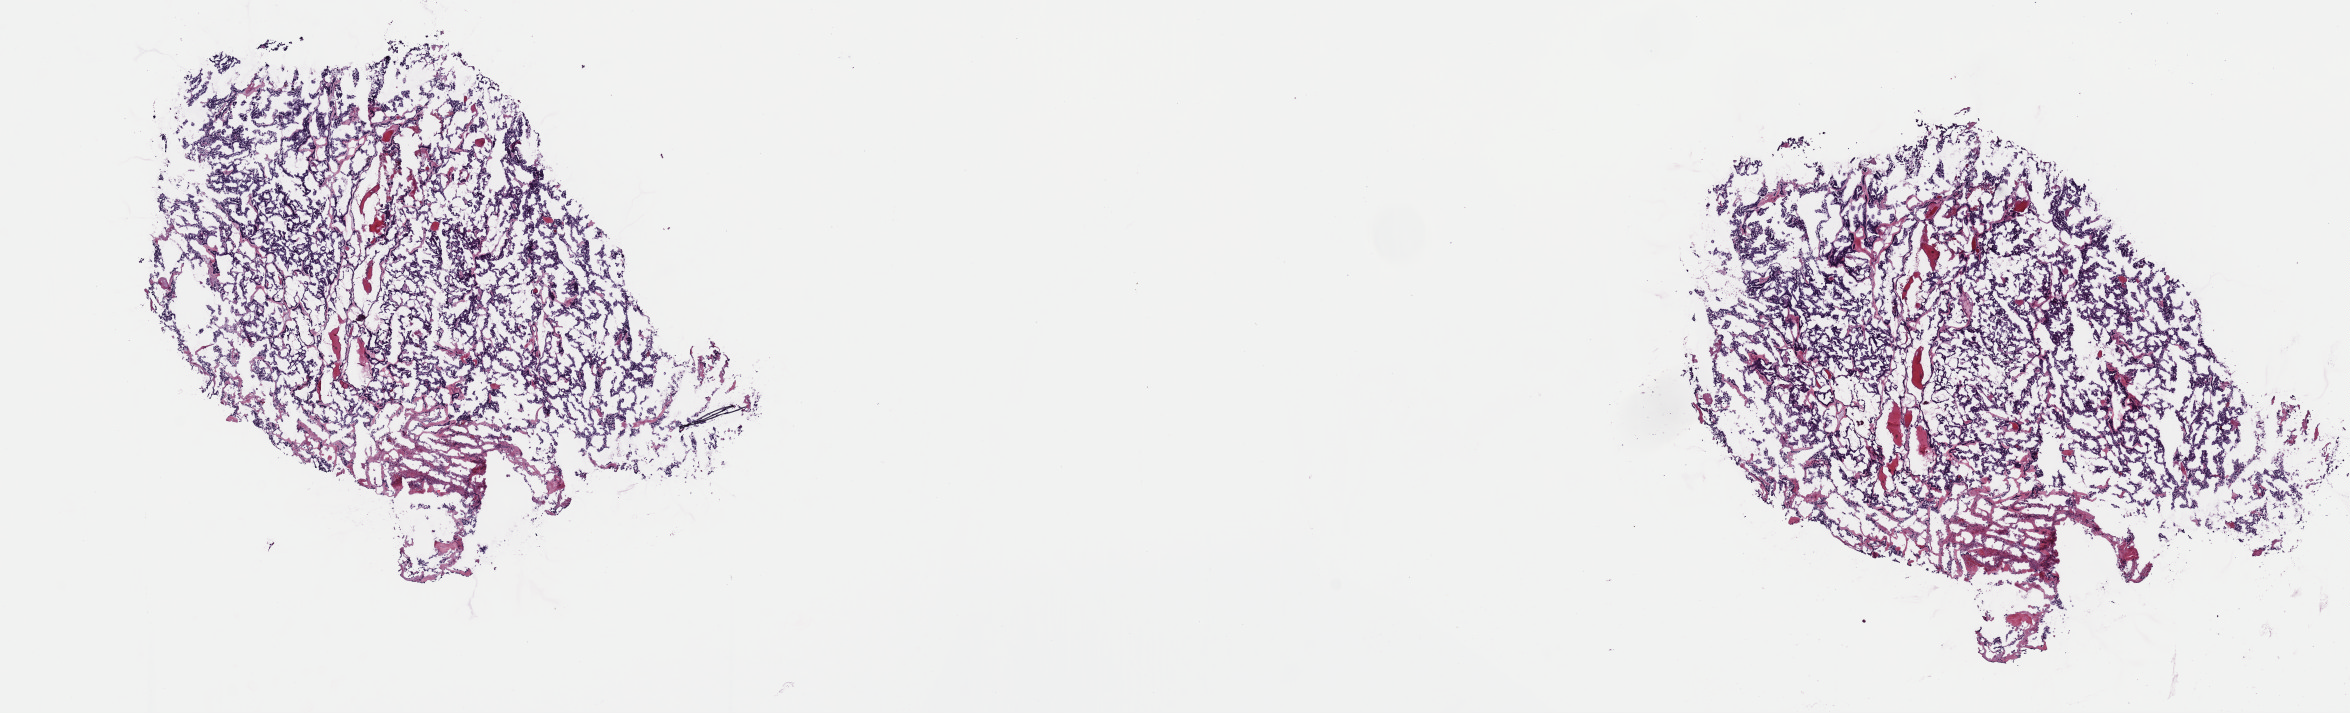
Digitized H&E tissue section (whole slide), low-resolution overview of the scanned area, about 18.6 x 5.6 mm. Frozen section. Thyroid, primary tumour sample. Male patient; age at initial diagnosis 75 years. Composition of this section per pathologist review: tumour cells 90%, tumour nuclei 80%, normal cells 0%, stromal cells 10%, necrosis 0%. Inflammatory infiltration, as recorded: lymphocyte infiltration 3%, monocyte infiltration 2%, neutrophil infiltration 0%.
• AJCC pathologic stage: IV (7th edition)
• diagnosis: Papillary adenocarcinoma, NOS (thyroid gland)
• laterality: right